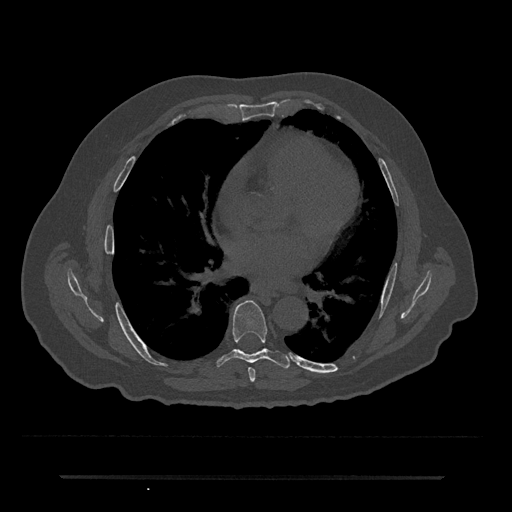
CT including the spine, one axial slice. Position 390 of 797 along the scan axis. Reconstruction kernel Br40s/3. 120 kVp. Bone window (W 1800 / L 400 HU). 512 × 512 image matrix, field of view 437 × 437 mm. Patient: male, 69 years. From the clinical record (not read from this slice): primary cancer: prostate.
Annotated regions visible in this slice (semi-automatically segmented with operator editing):
- T6 vertebra: bounding box (x1, y1, x2, y2) in pixels: (248, 367, 256, 382)
- T7 vertebra: (216, 300, 290, 369)